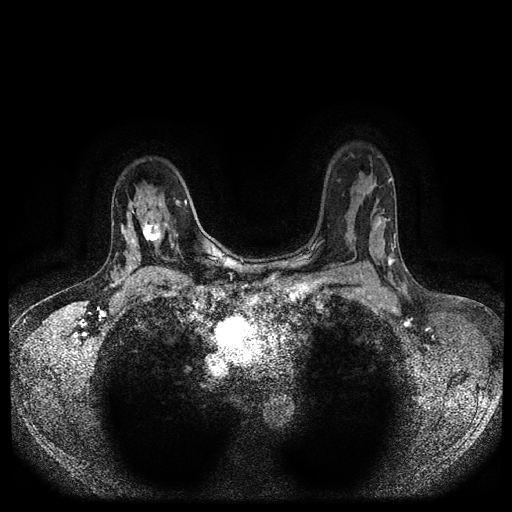
Breast MRI (dynamic contrast-enhanced, multi-phase), one axial slice. Slice 71 of 116 in the series (ordered by position). Dynamic contrast-enhanced series, time point 2 of 5 at this slice position (early post-contrast). 1.5 T. TE 2.6 ms, TR 5.4 ms. 512 × 512 image matrix, field of view 340 × 340 mm. Patient: female, 47 years.
Annotated regions visible in this slice (semi-automatic segmentation, software-assisted and operator-edited):
- breast lesion (labelled 'tumour' in the annotation; benign lesions carry a separate 'benign' label): box from (x=141, y=214) to (x=165, y=248) px